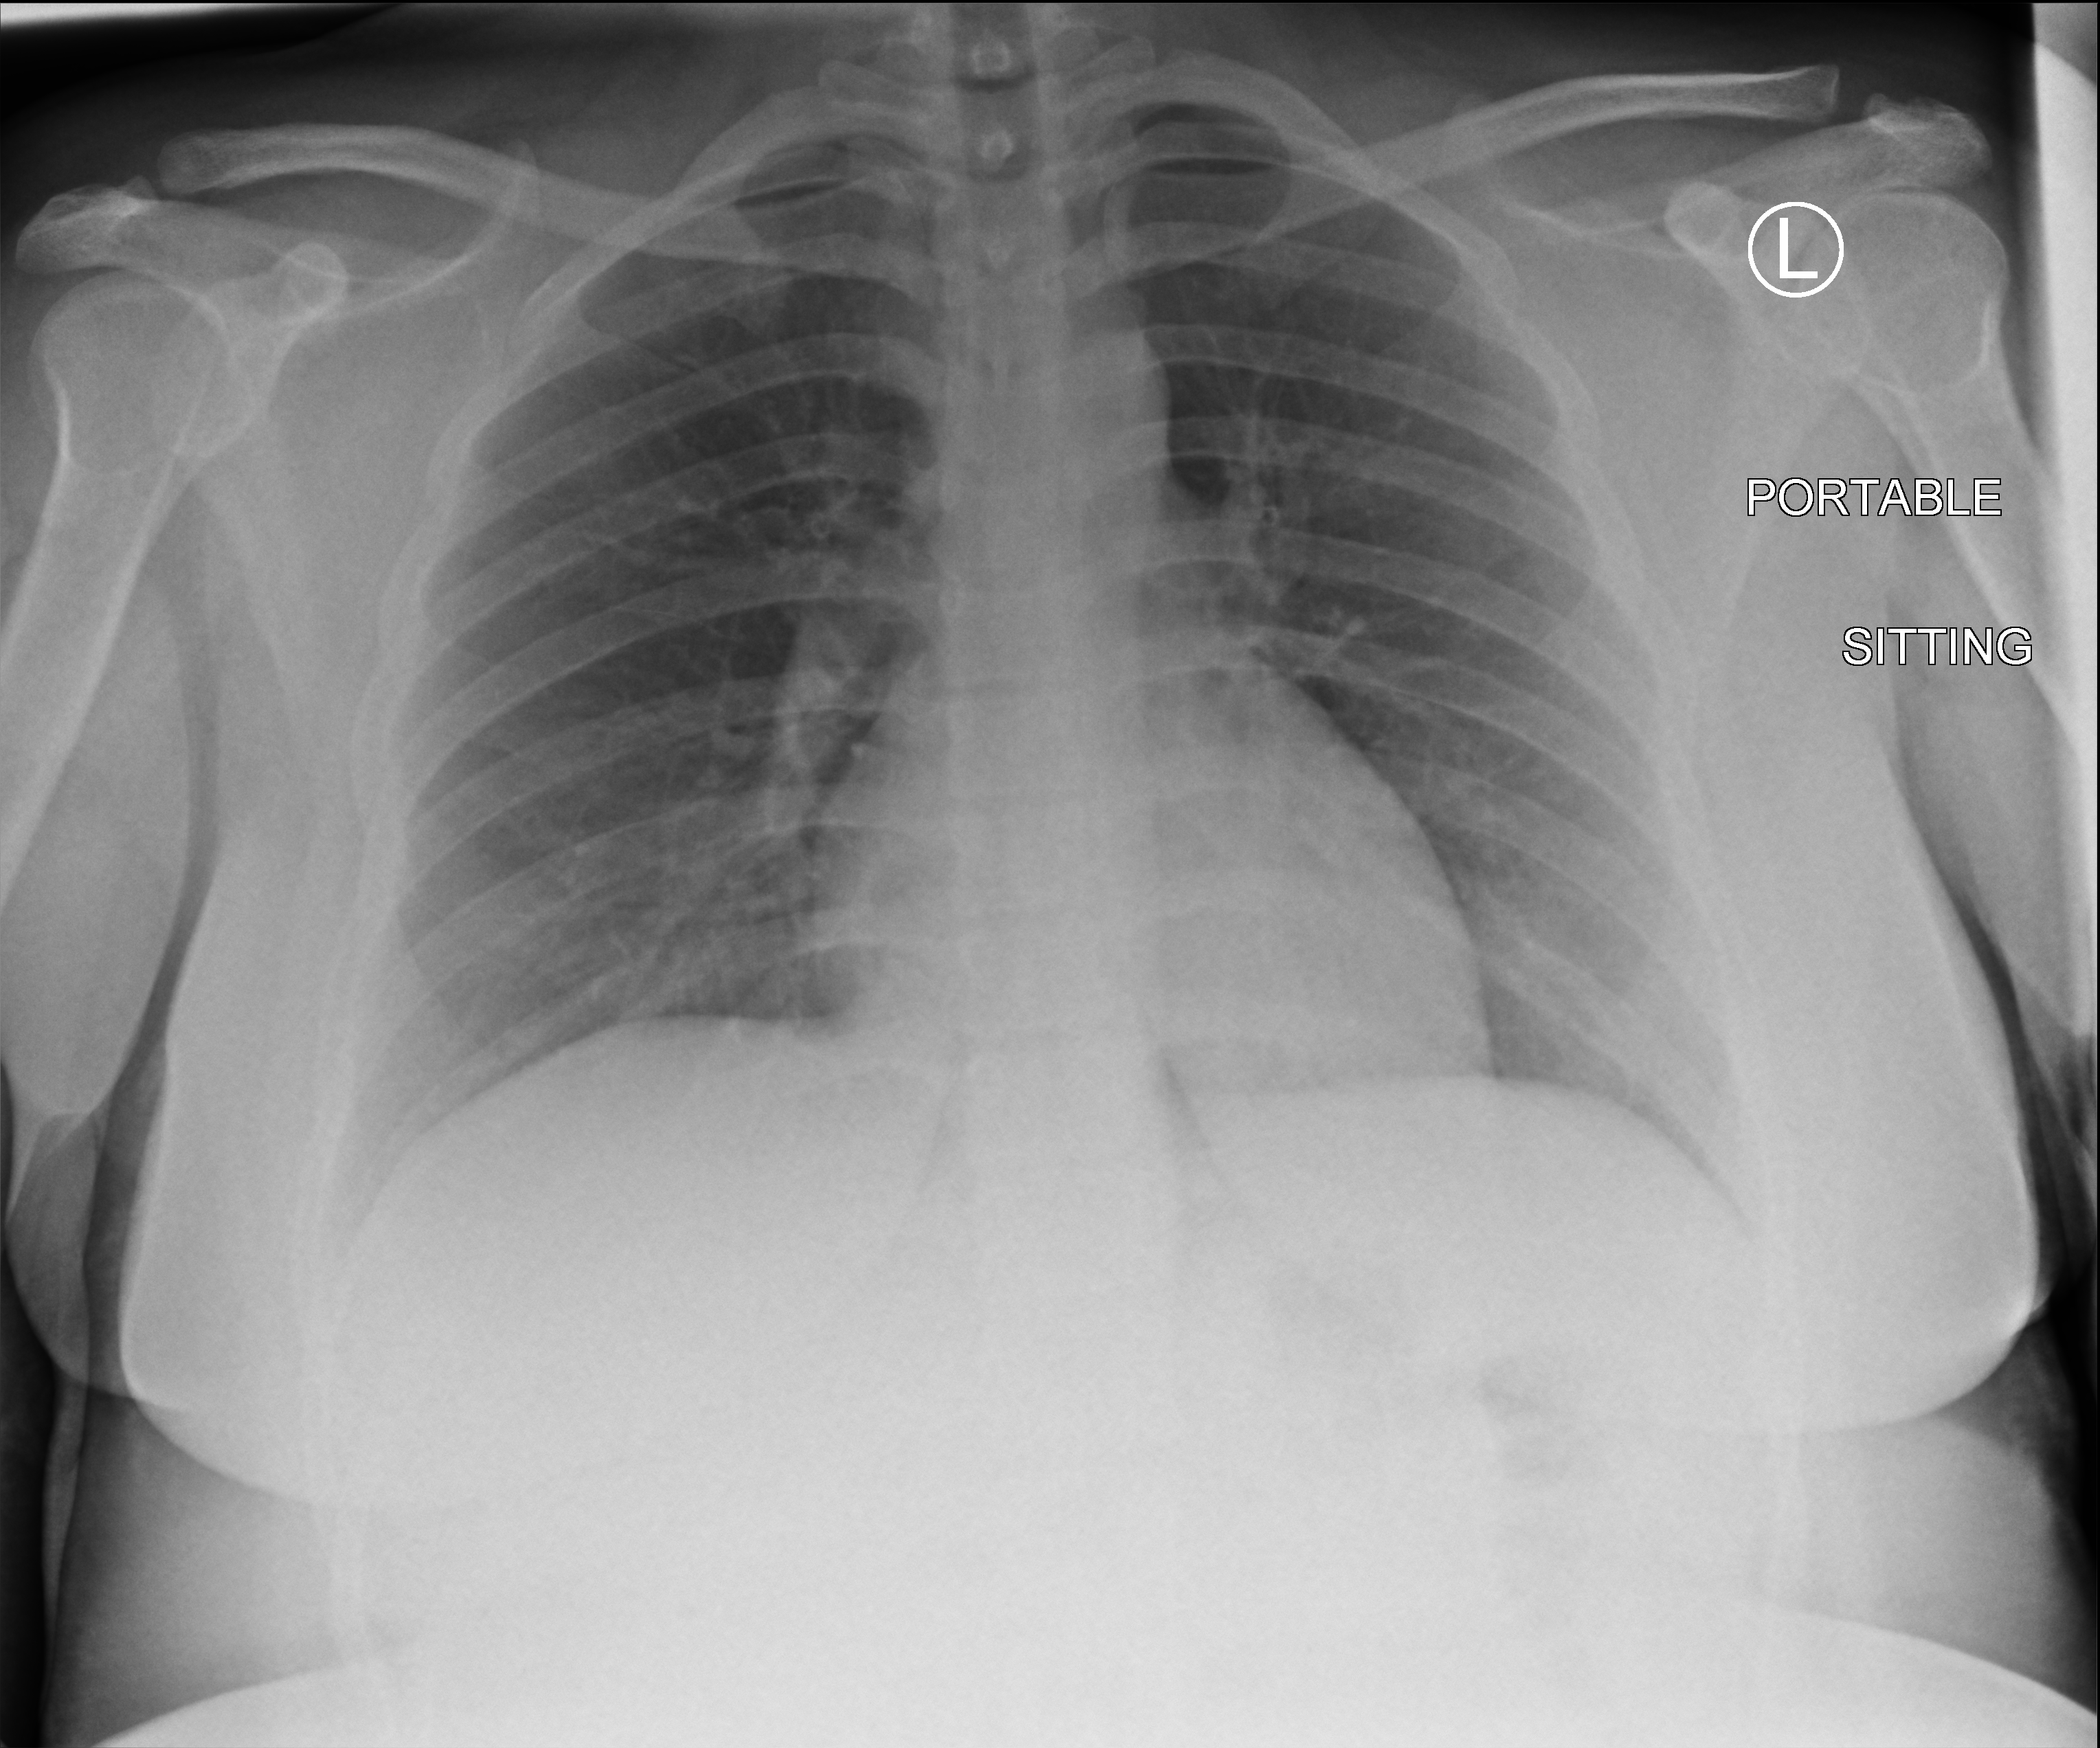
Chest X-ray (portable), anteroposterior (AP) projection. Patient hospitalised with COVID-19; female, aged 18–59 years.
From the hospital-stay record, not from the radiograph (when in the stay this image was taken is not recorded): hypertension (admission record): no.